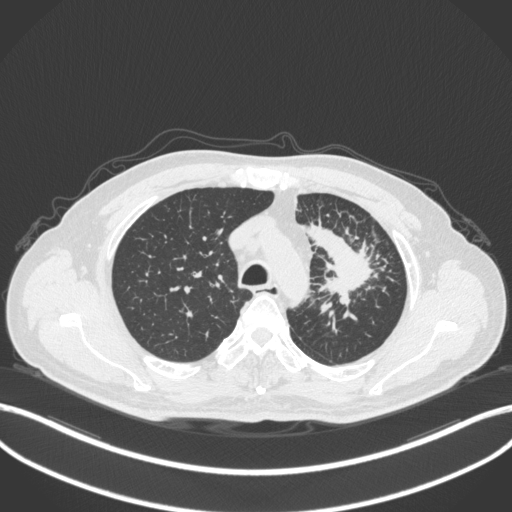
Chest CT, one axial slice. Slice 271 of 386 in the series (ordered by position). 120 kVp. Lung window (W 1500 / L -600 HU). 1 mm slice thickness. 512 × 512 image matrix, field of view 400 × 400 mm. Patient: male, 69 years. Case-level facts recorded for this patient, not image findings: clinical TNM (as recorded): T2a N2 M0.
Outlined on this slice (rectangle marked by the reading radiologist):
- lung tumour (recorded histology: adenocarcinoma): bounding box [x1, y1, x2, y2] px = [304, 217, 381, 306]